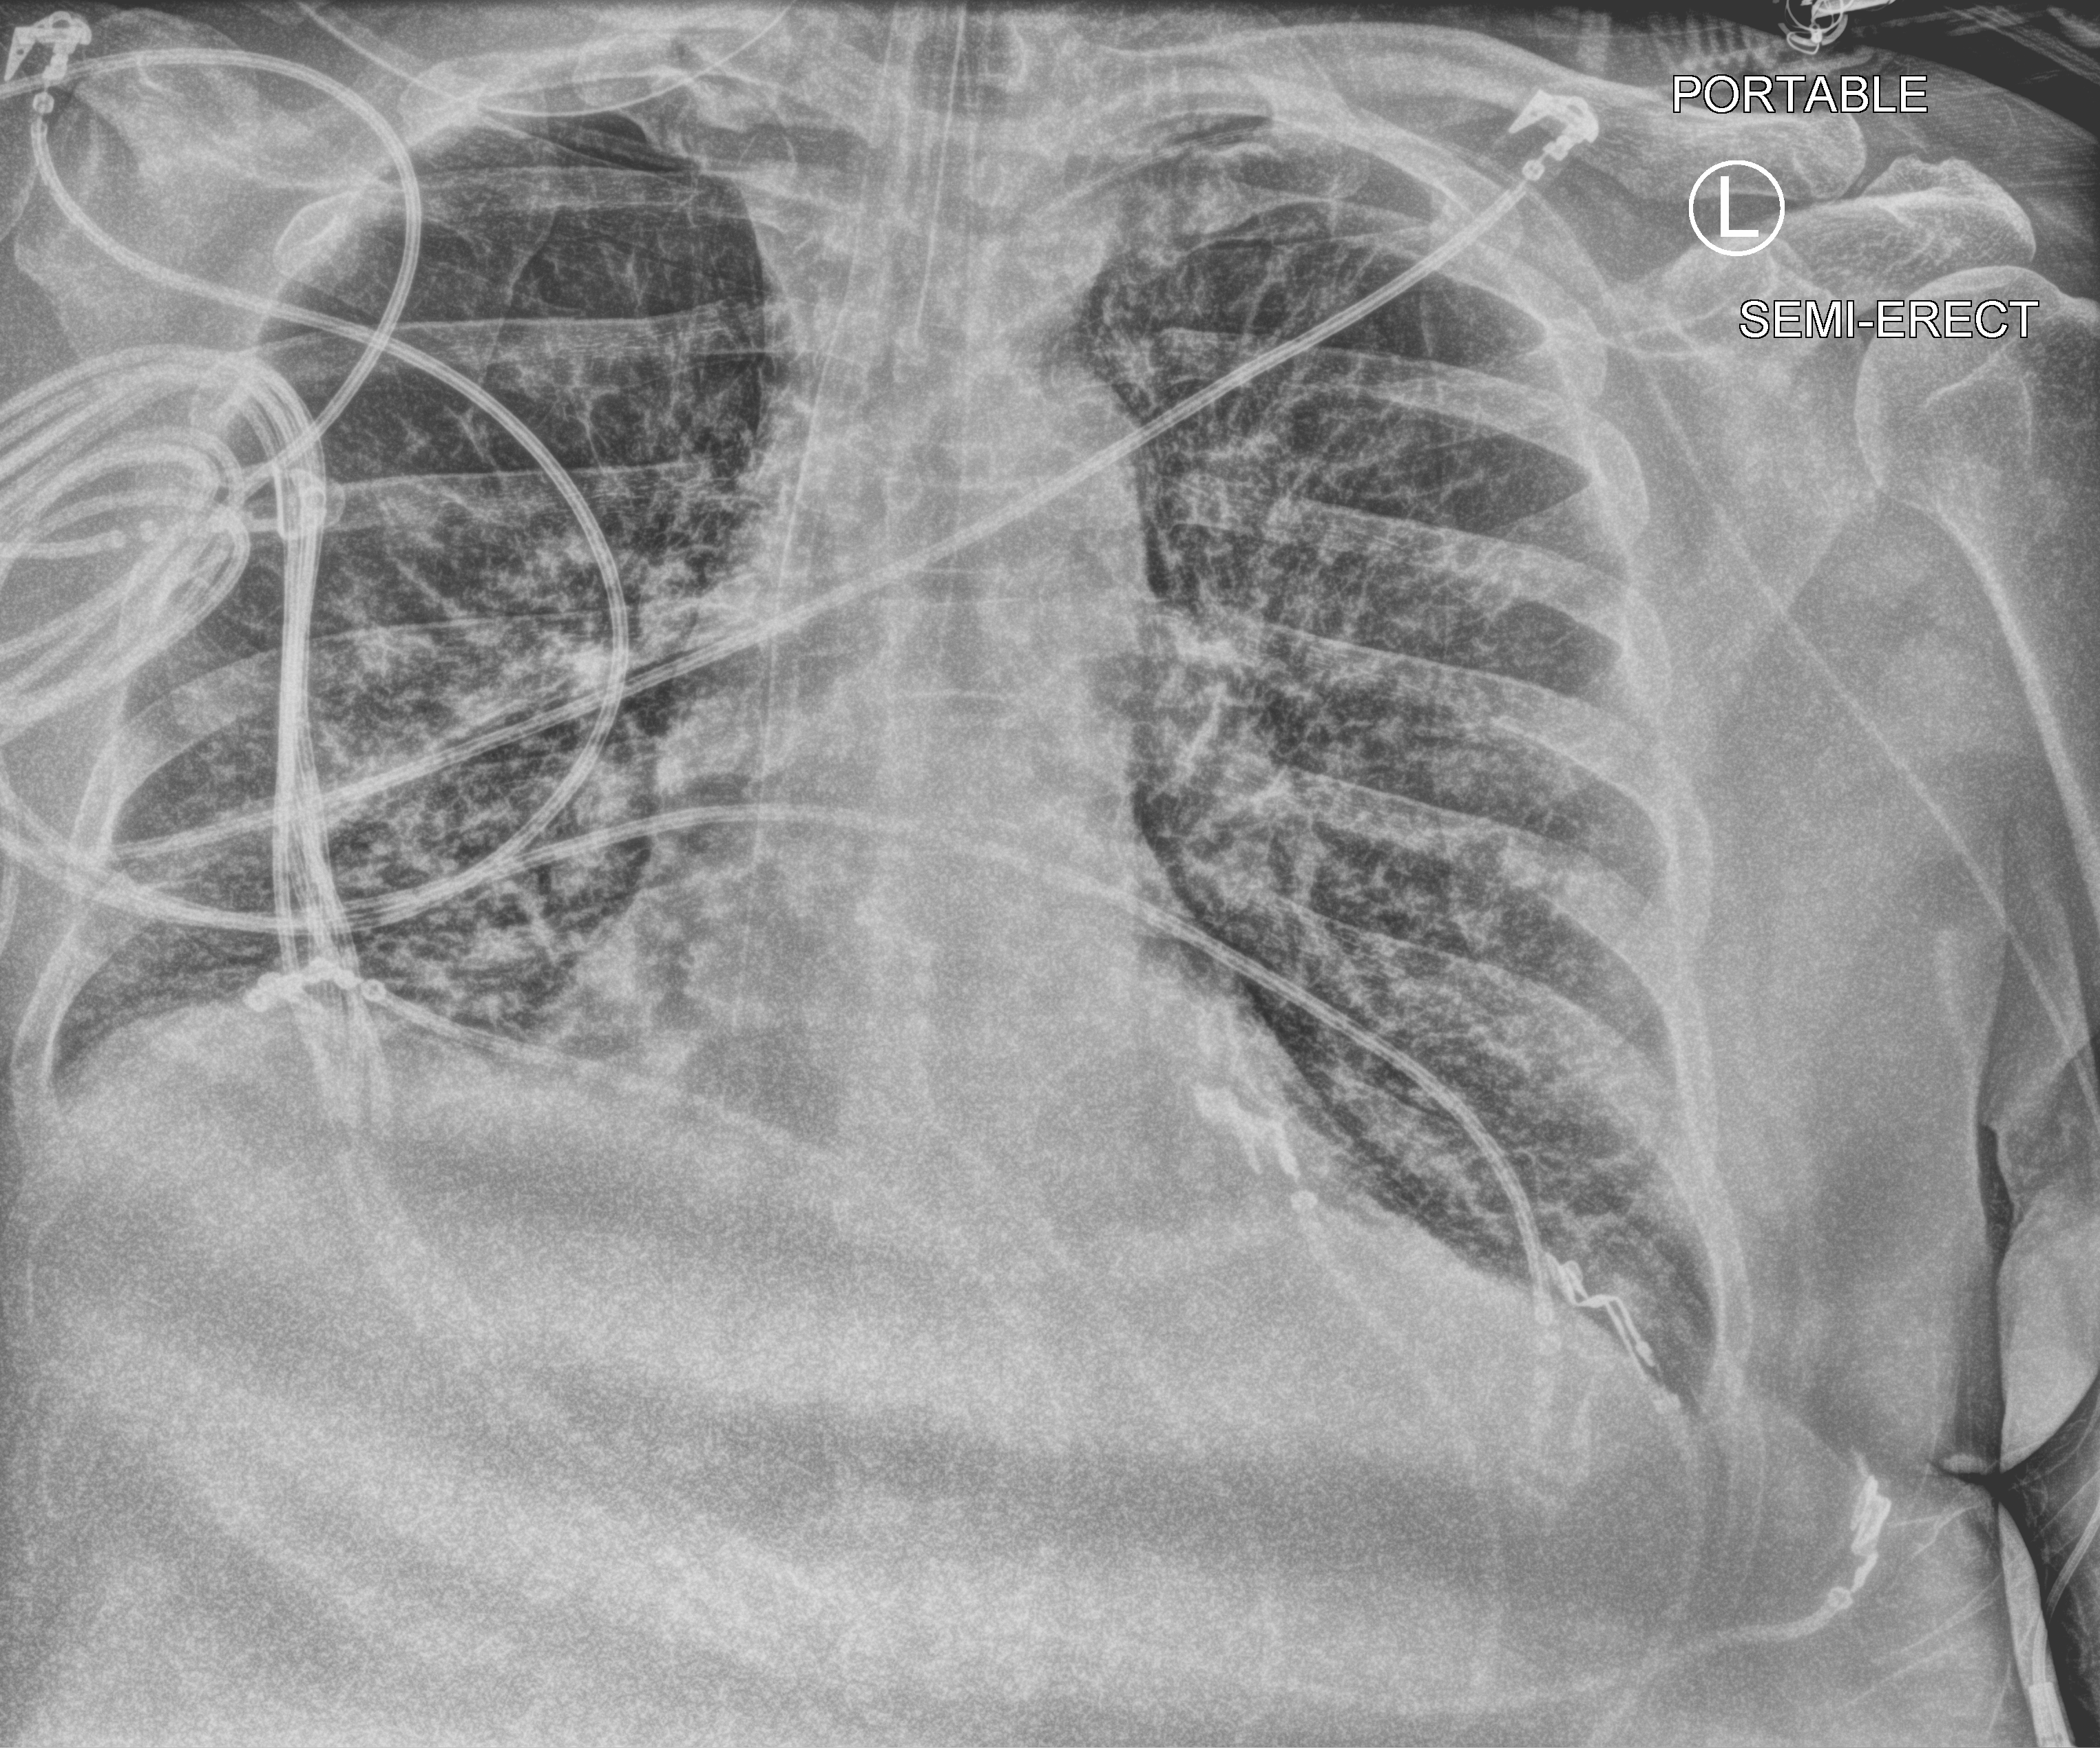
Portable chest radiograph, anteroposterior (AP) projection. Patient hospitalised with COVID-19, aged 18–59 years.
Hospital-stay facts (about this admission, not read from this image; timing relative to this image not recorded):
- admitted to intensive care during this hospital stay: yes